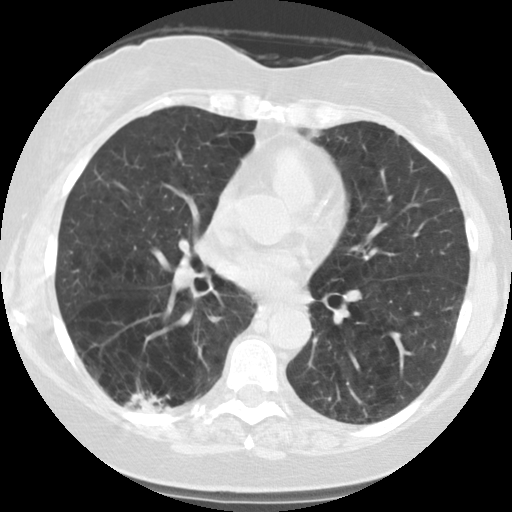
Low-dose screening chest CT, one axial slice; slice 57 of 122 in the series (ordered by position); 140 kVp; lung window (W 1500 / L -600 HU); 512 × 512 image matrix, field of view 310 × 310 mm.
Outlined on this slice (expert manual segmentation):
- lesion 1 (tumor, lower lobe of right lung): bounding box (x1, y1, x2, y2) in pixels: (125, 387, 164, 413)